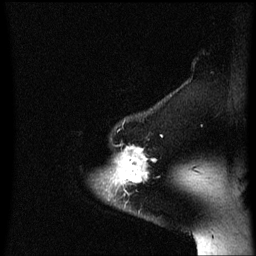
Breast MRI (dynamic contrast-enhanced), one sagittal slice; position 53 of 60 along the scan axis; dynamic contrast-enhanced series, image 2 of 3 at this slice position (ordered by acquisition); 1.5 T; TE 4.2 ms, TR 8.4 ms; 2 mm slice thickness; 256 × 256 image matrix, field of view 200 × 200 mm. Female patient, age 54 years. Case-level facts recorded for this patient, not image findings: setting: breast cancer imaged before/during neoadjuvant chemotherapy; receptor status: HR-positive, HER2-negative.
Annotated regions visible in this slice (semi-automatic segmentation, software-assisted and operator-edited):
- analysis volume of interest (the breast-tissue region the enhancement analysis was run in; not a lesion): bounding box (x1, y1, x2, y2) in pixels: (104, 146, 159, 199)
- tumour enhancement mask (voxels above the 70 % enhancement threshold inside the analysis volume of interest): (108, 146, 157, 191)